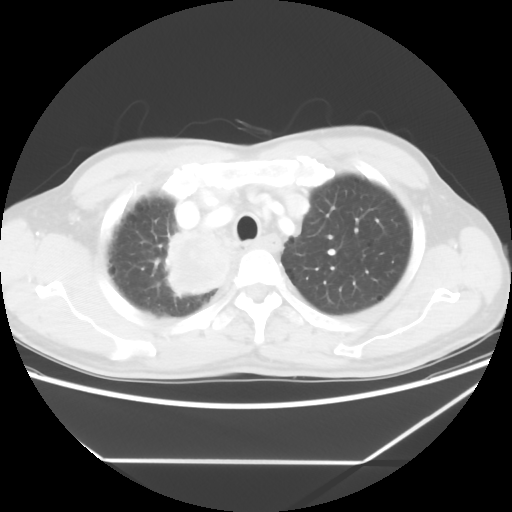
Chest CT, one axial slice; slice 50 of 60 in the series (ordered by position); reconstruction kernel STANDARD; 120 kVp; lung window (W 1500 / L -600 HU); 5 mm slice thickness; 512 × 512 image matrix, field of view 367 × 367 mm. Male patient, age 58 years. From the clinical record (not read from this slice): clinical TNM (as recorded): T2 N2 M0.
Structures marked on this image (bounding box drawn by a radiologist):
- lung tumour (recorded histology: squamous cell carcinoma): box from (x=160, y=228) to (x=228, y=302) px